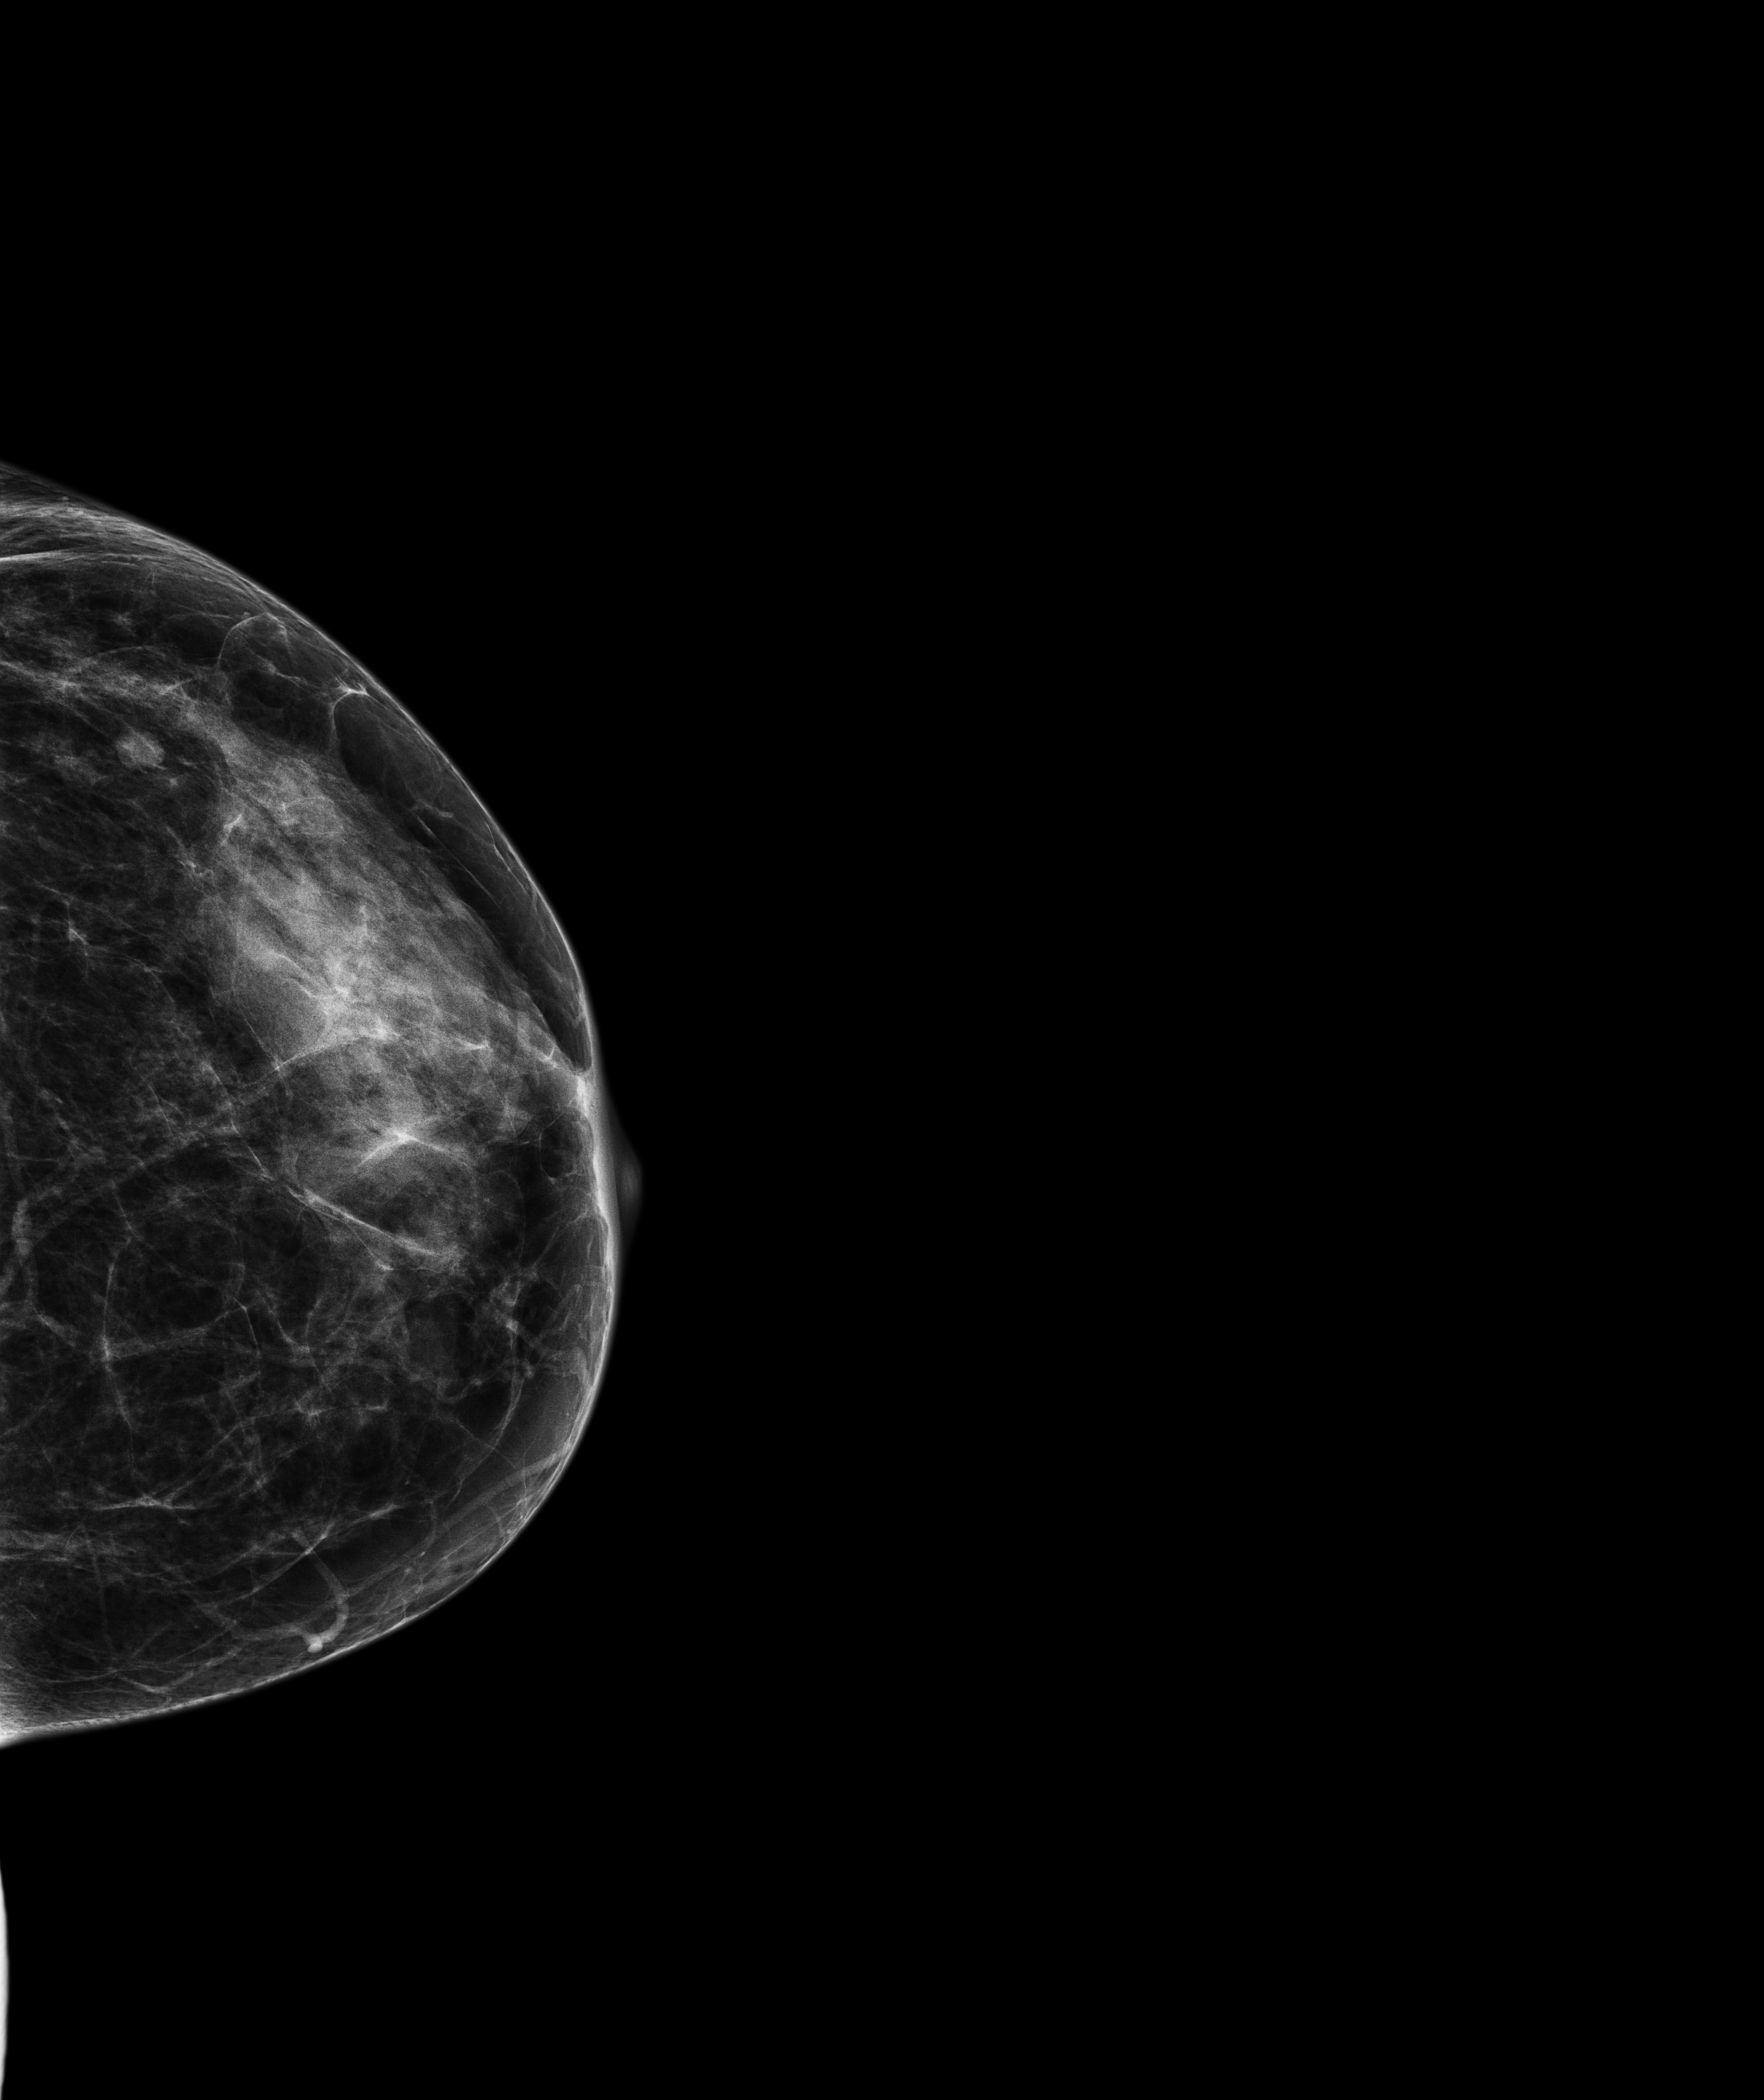
Screening examination, compressed breast thickness 28.9 mm. Patient aged 47 years (female).
Image type: full-field digital mammogram. Breast: left. Projection: CC view. BI-RADS breast density category at the screening exam (both breasts, scale 1–4): 3. Final BI-RADS assessment for this screening round (tomosynthesis exam, both breasts): category 2. Recall: no recall after this screen.